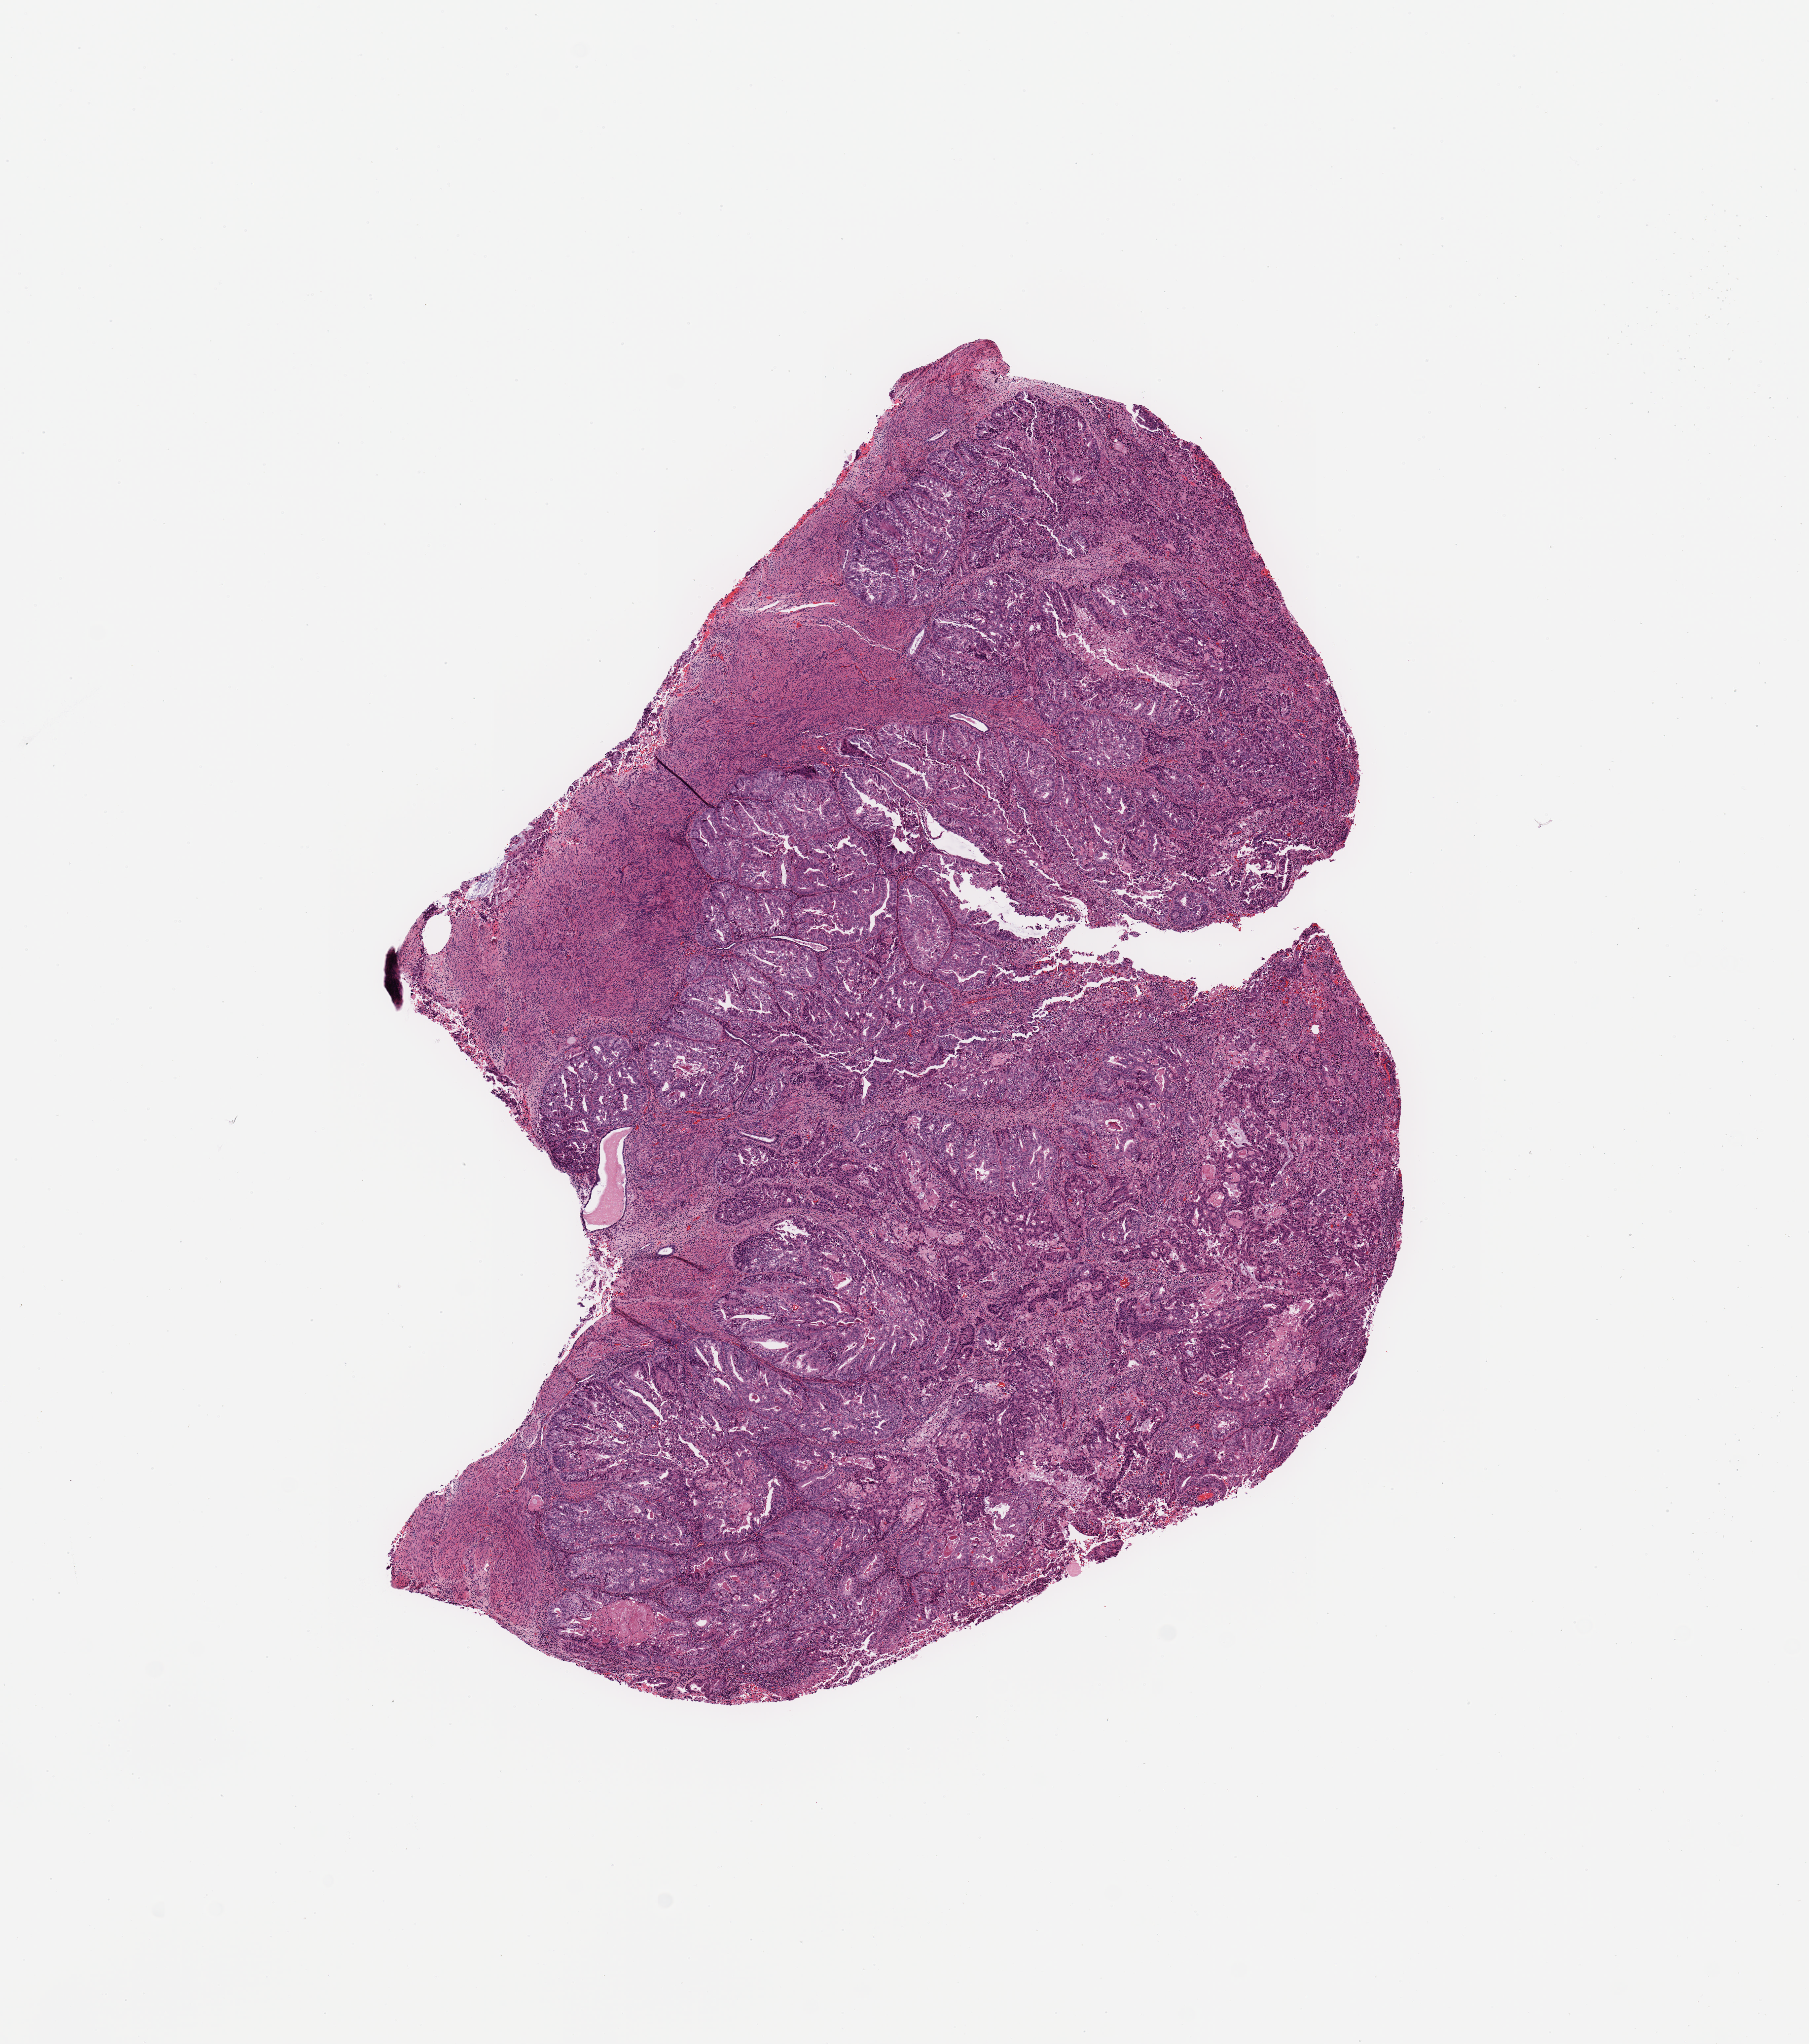
Hematoxylin and eosin (H&E) stained whole-slide image, a low-resolution overview of the entire scanned area, about 10.8 x 12.2 mm (slide scanned at 20x). Tumour tissue sample, uterus. Patient: female, age 74 years. Histologic grade: G3 (poorly differentiated).
Histologic diagnosis: Endometrioid adenocarcinoma, NOS. AJCC pathologic stage: IV.